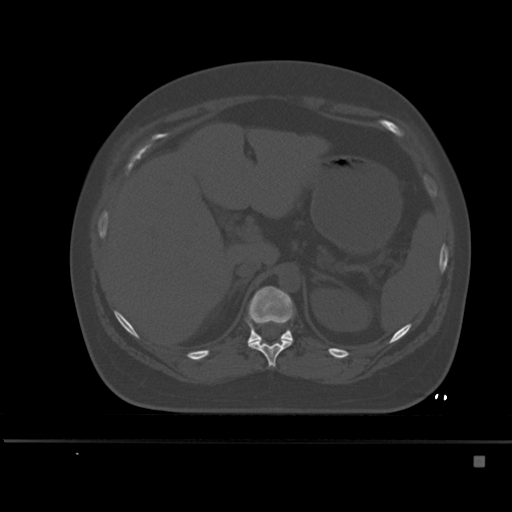
CT including the spine, one axial slice; bone window (W 1800 / L 400 HU); 1.5 mm slice thickness; 512 × 512 image matrix, field of view 404 × 404 mm. Female patient, age 33 years. Case-level facts recorded for this patient, not image findings: primary cancer: breast; vertebrae with lytic lesions (as recorded): T1.
Structures marked on this image (semi-automatically segmented with operator editing):
- T11 vertebra: bounding box (x1, y1, x2, y2) in pixels: (248, 338, 293, 367)
- T12 vertebra: (247, 286, 294, 344)